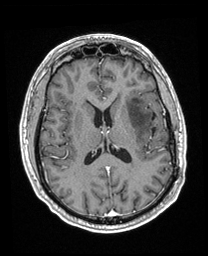
Brain MRI from a brain-tumour surgery series, one axial slice; slice 98 of 208 in the series (ordered by position); T1-weighted post-contrast; 1 mm slice thickness; 208 × 256 image matrix, field of view 211 × 260 mm. Case-level facts recorded for this patient, not image findings: histopathology: Astrocytoma; WHO grade: 3; IDH mutation: yes; tumour location: Left Insular.
Structures marked on this image (outlined manually by an expert reader):
- previous resection cavity: box from (x=151, y=113) to (x=156, y=137) px